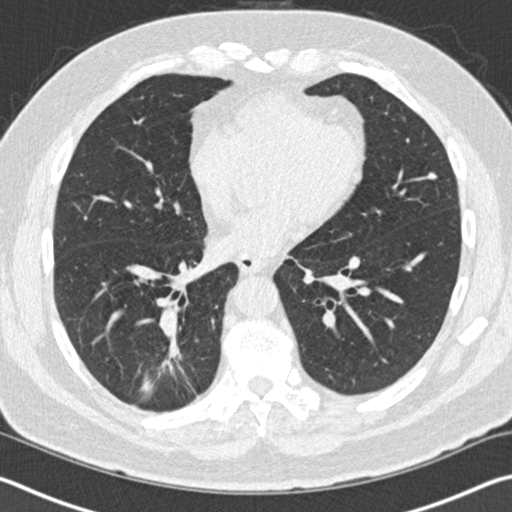
Low-dose screening chest CT, one axial slice; slice 47 of 141 in the series (ordered by position); reconstruction kernel B30f; lung window (W 1500 / L -600 HU); 2 mm slice thickness; 512 × 512 image matrix.
Structures marked on this image (outlined manually by an expert reader):
- lesion 1 (tumor, lower lobe of right lung): bounding box (x1, y1, x2, y2) in pixels: (160, 334, 183, 375)